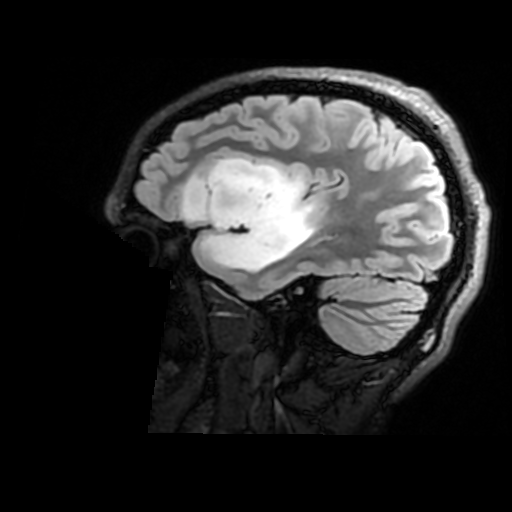
Brain MRI from a brain-tumour surgery series, one sagittal slice; slice 126 of 176 in the series (ordered by position); T2 FLAIR; 1 mm slice thickness; 512 × 512 image matrix. From the clinical record (not read from this slice): histopathology: Astrocytoma; WHO grade: 2; IDH mutation: yes.
Annotated regions visible in this slice (expert manual segmentation):
- tumour: bounding box <183,157,317,273> (left, top, right, bottom; pixels)